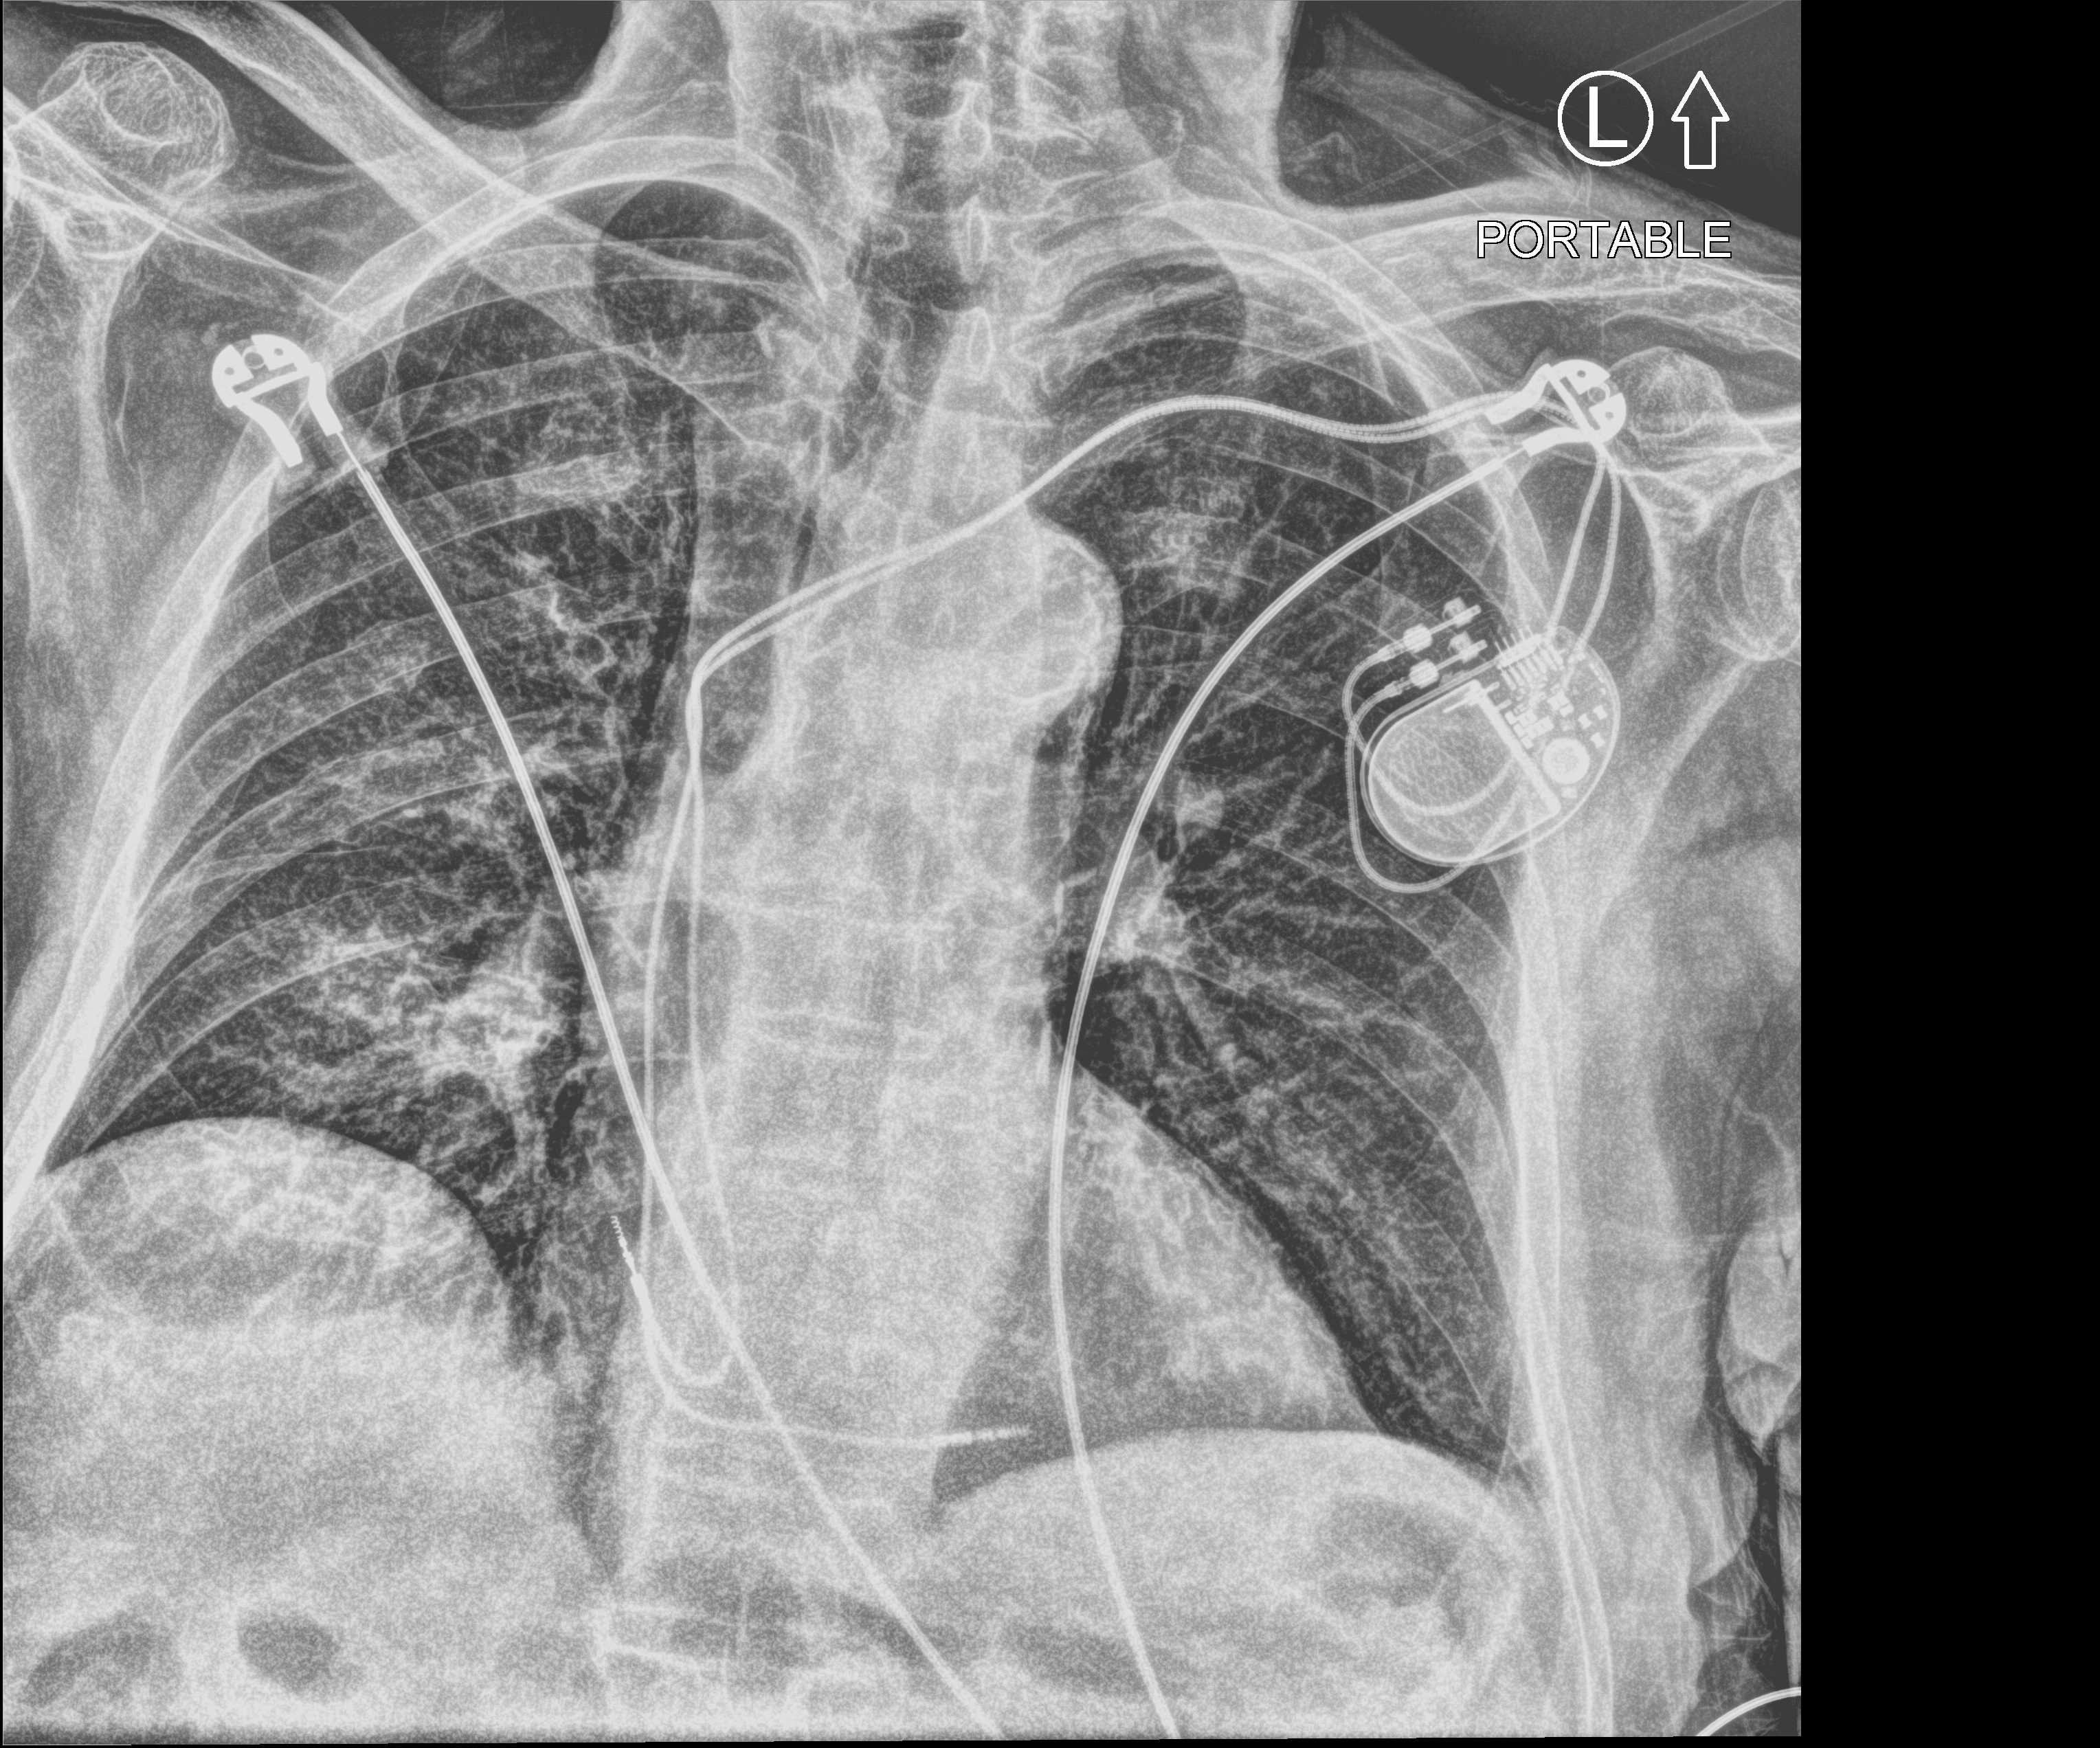
Bedside chest radiograph (computed radiography), anteroposterior (AP) projection. Patient hospitalised with COVID-19; male, aged 75–90 years.
From the hospital-stay record, not from the radiograph (when in the stay this image was taken is not recorded): admitted to intensive care during this hospital stay: no.